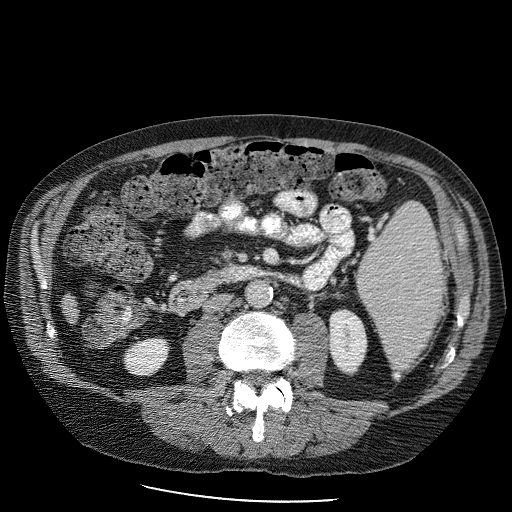
Contrast-enhanced abdominal CT (liver protocol), one axial slice. Soft-tissue window (W 400 / L 40 HU). 512 × 512 image matrix. From the clinical record (not read from this slice): diagnosis: hepatocellular carcinoma (patient treated with transarterial chemoembolisation; whether this scan precedes or follows treatment is not stated here); TNM stage (as recorded): Stage-II.
Annotated regions visible in this slice (semi-automatic segmentation, software-assisted and operator-edited):
- liver parenchyma outside the tumour (the mass and vessels are separate outlines, so this box may not span the whole liver): bounding box (x1, y1, x2, y2) in pixels: (60, 288, 78, 322)